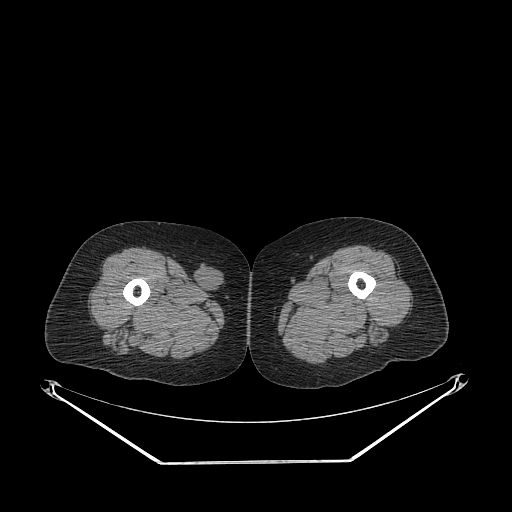
CT of an extremity soft-tissue mass (from a PET/CT study), one axial slice; position 243 of 311 along the scan axis; 140 kVp; soft-tissue window (W 400 / L 40 HU); 3.75 mm slice thickness; 512 × 512 image matrix, field of view 500 × 500 mm. Female patient. From the clinical record (not read from this slice): histological type: leiomyosarcoma; grade: intermediate; site of the primary tumour: parascapusular.
Structures marked on this image (expert contour drawn on MRI and transferred to this co-registered scan by the dataset authors):
- gross tumour volume including surrounding oedema: bounding box (x1, y1, x2, y2) in pixels: (194, 262, 225, 293)
- gross tumour volume (mass): (196, 262, 223, 287)